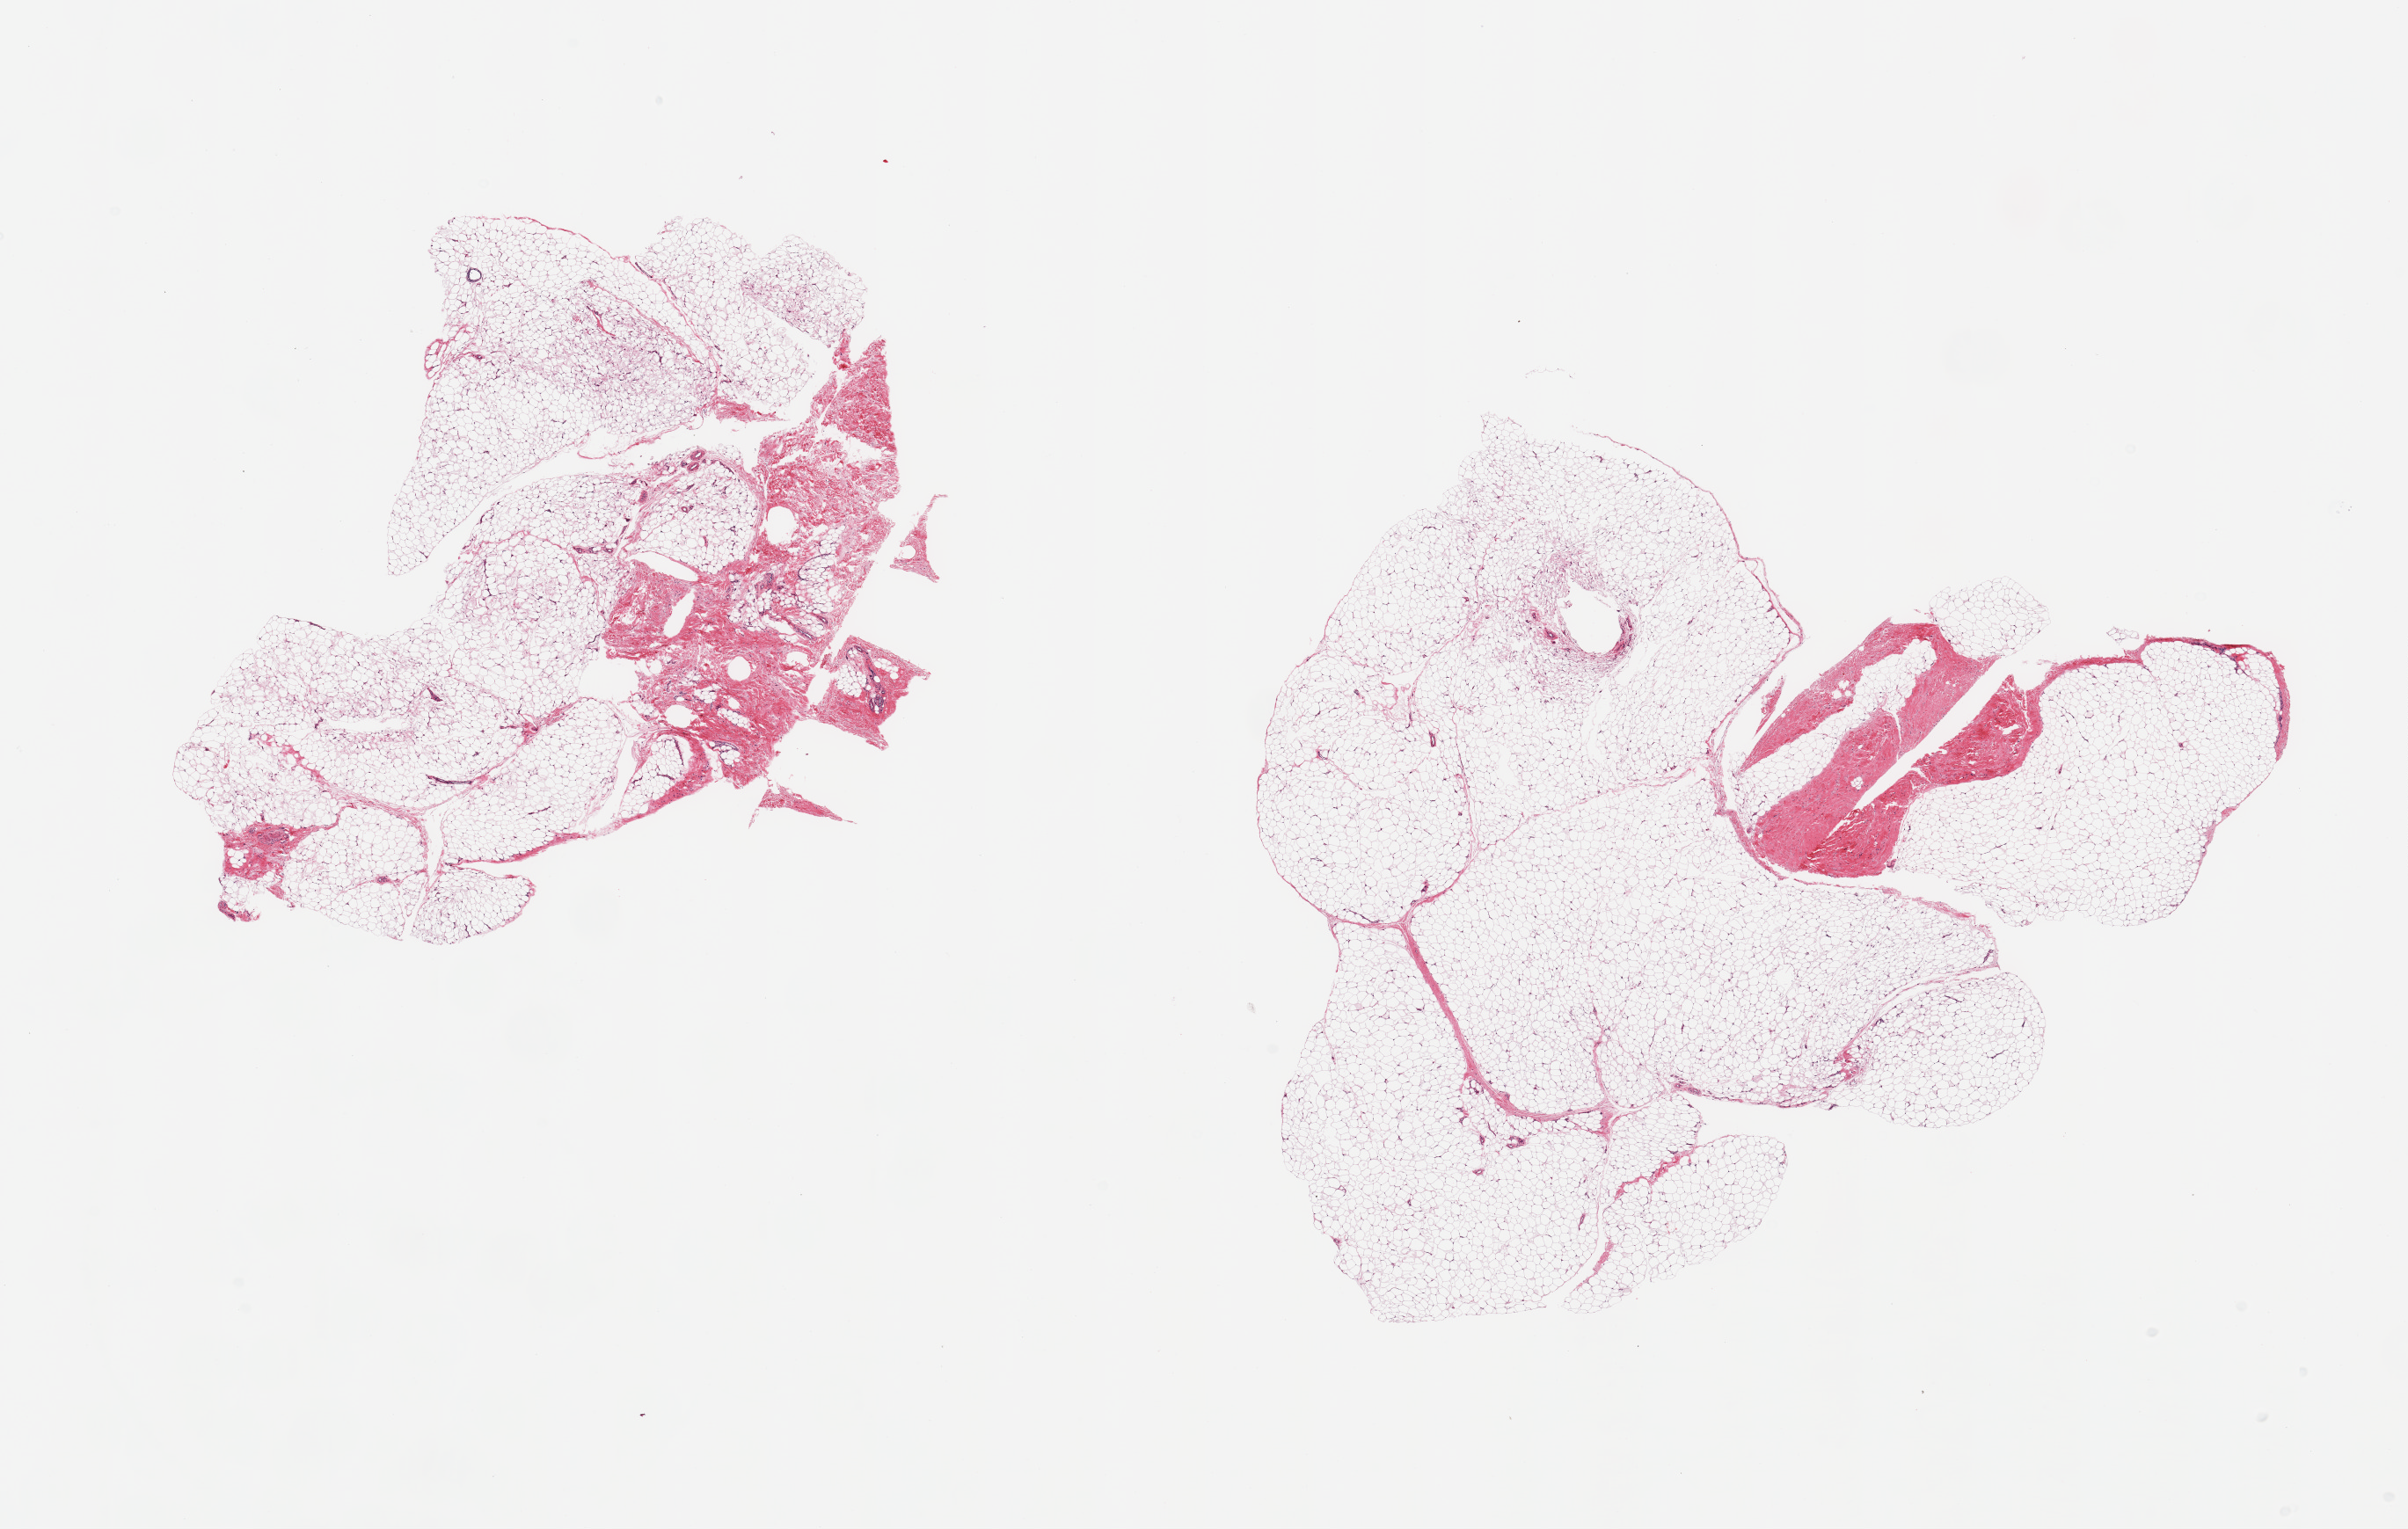
Whole-slide image, H&E stain — a low-resolution overview of the entire scanned area, about 21.7 x 13.8 mm. PAXgene-fixed paraffin-embedded (PFPE) section. Section of adipose tissue (target tissue). Tissue donor sample. Female donor.
Reviewer comment on this tissue sample: 2 pieces; 10% fibrous content.